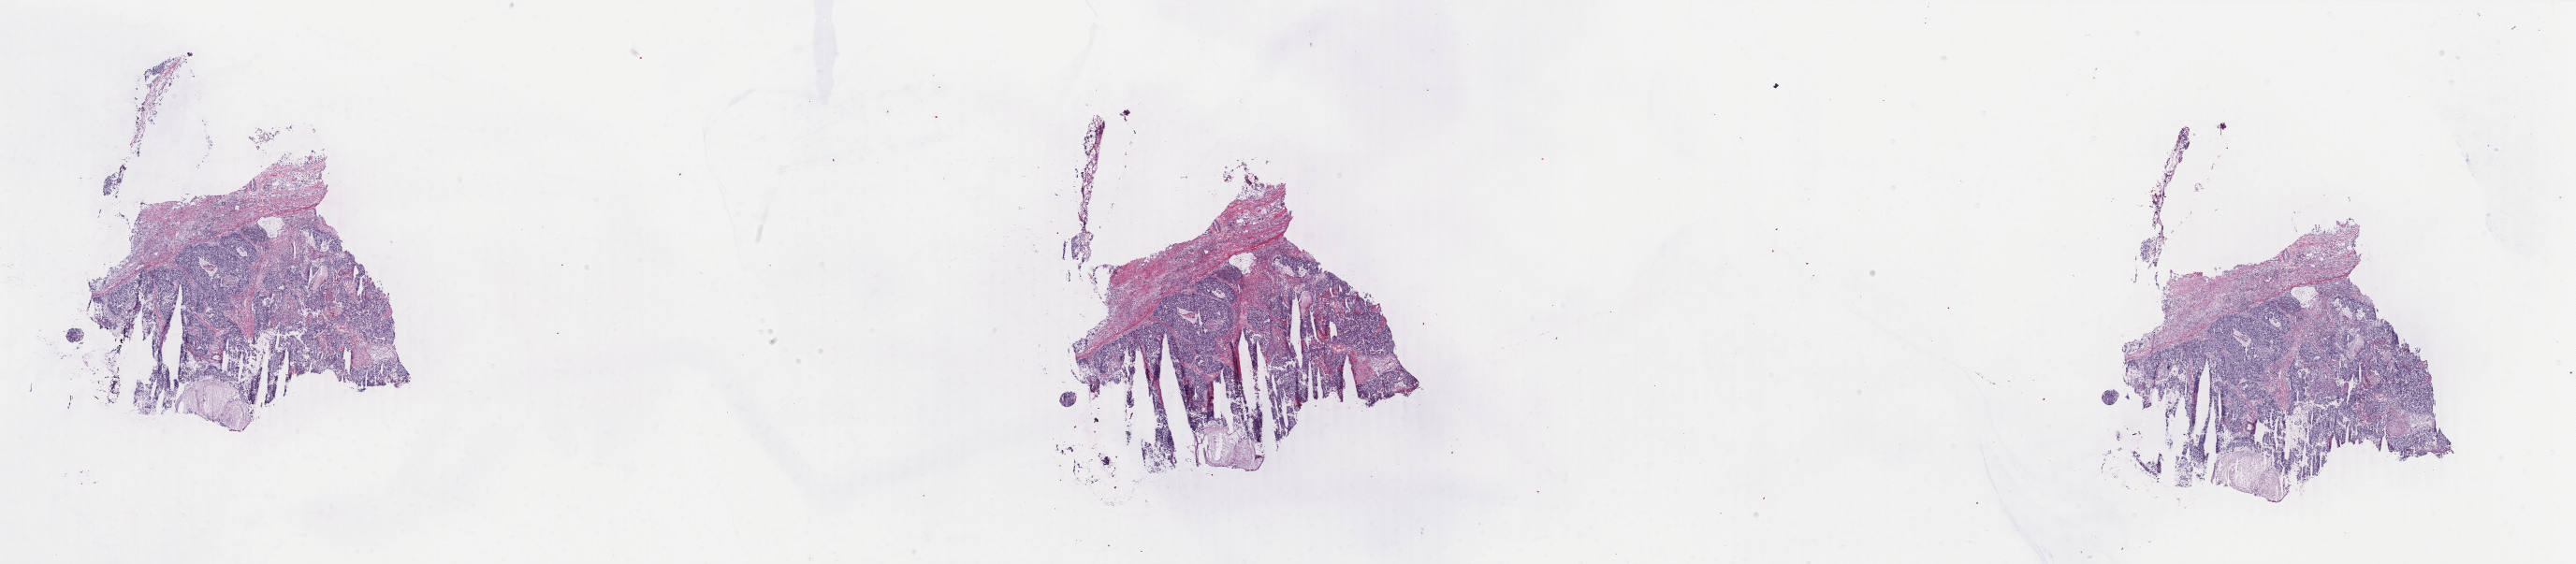
H&E whole-slide image, low-resolution overview of the scanned area, about 43.8 x 9.6 mm (acquisition: 40x scan), frozen section, primary tumour sample from the breast. Female patient; age at initial diagnosis 59 years. Composition of this section per pathologist review: tumour cells 75%, tumour nuclei 70%, normal cells 0%, stromal cells 15%, necrosis 10%. Infiltration values recorded for this section: lymphocyte infiltration 0%, monocyte infiltration 0%, neutrophil infiltration 0%.
AJCC pathologic stage: IIIA. Lymph nodes positive (case pathology): 7 of 26 examined. Pathologic diagnosis: Infiltrating duct carcinoma, NOS.